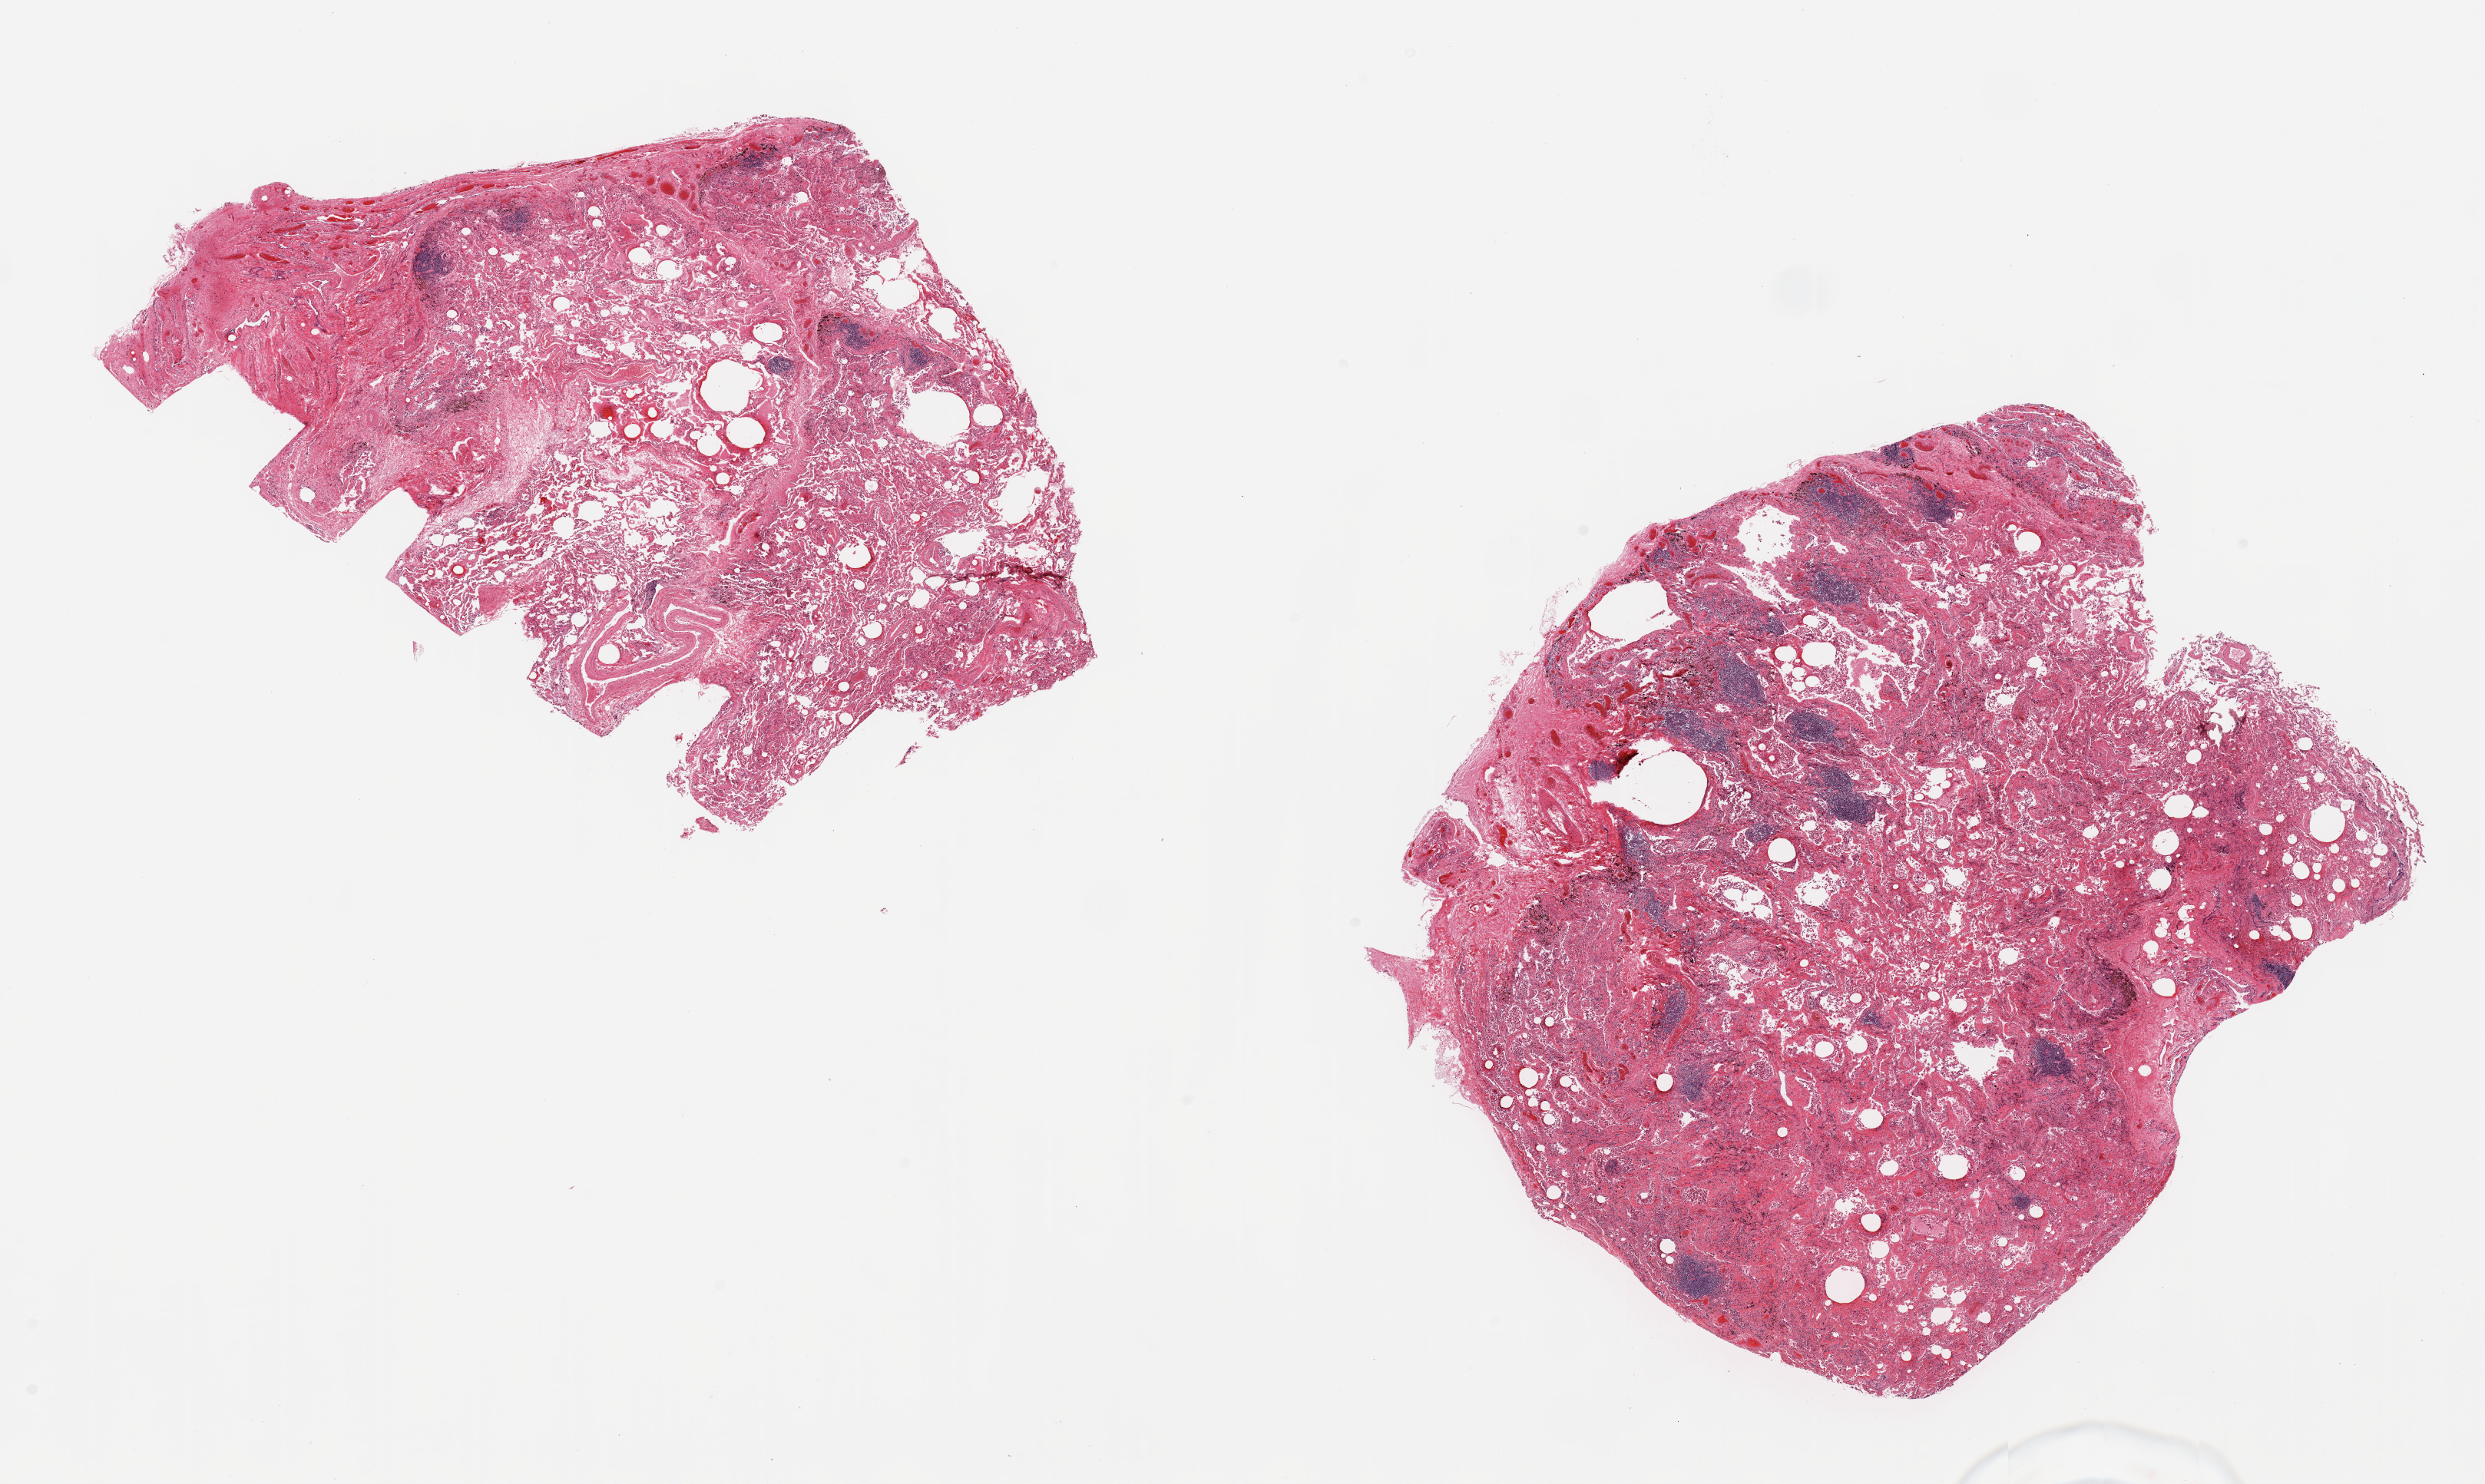
Digitized haematoxylin and eosin-stained section, low-resolution overview of the scanned area, about 25.6 x 15.3 mm (slide scanned at 20x); PAXgene-fixed paraffin-embedded (PFPE) section; sampled site (target tissue): lung; tissue donor sample. Donor: male.
Reviewer comment on this tissue sample: 2 pieces, marked DAD-type process with fibrin/chronic pneunonitits.